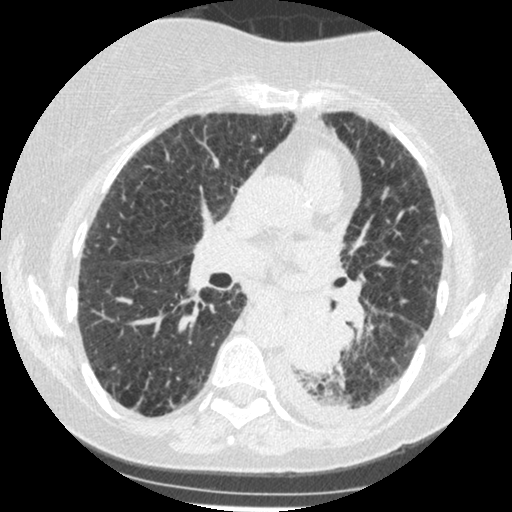
Chest CT (low-dose screening protocol), one axial image. Third screening round (two years after baseline). Lung window (W 1500 / L -600 HU). Standard (soft-tissue) reconstruction kernel (STANDARD). Slice 208 of 341 in the series. 512 × 512 image matrix. Female, age 60 years at enrolment.
Lesion marked by an expert reader, bounding box [x1, y1, x2, y2] px = [272, 306, 342, 374]. Screening reader's record for this exam (one nodule recorded; not confirmed to be the boxed lesion): non-calcified nodule or mass ≥4 mm, left lower lobe, 54 × 38 mm, smooth margins, soft tissue attenuation, pre-existing on the prior screen: yes; interval growth: yes. Official screen result: positive, other. Lung cancer was diagnosed 15 days after this screen: small cell carcinoma, NOS, left lower lobe, undifferentiated (G4), stage IV (AJCC 6th edition), 69 mm at pathology.